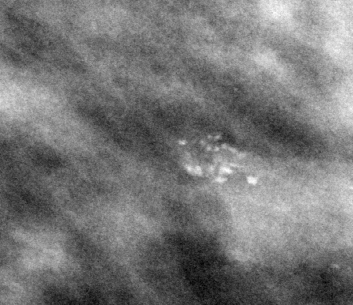
Region of interest cut from a scanned film mammogram (one marked finding); left breast; MLO view; BI-RADS breast density category 2 (scale 1–4).
Finding: calcifications, morphology pleomorphic, distribution clustered; BI-RADS assessment category 4; pathology result (as recorded, not read from the image): benign.